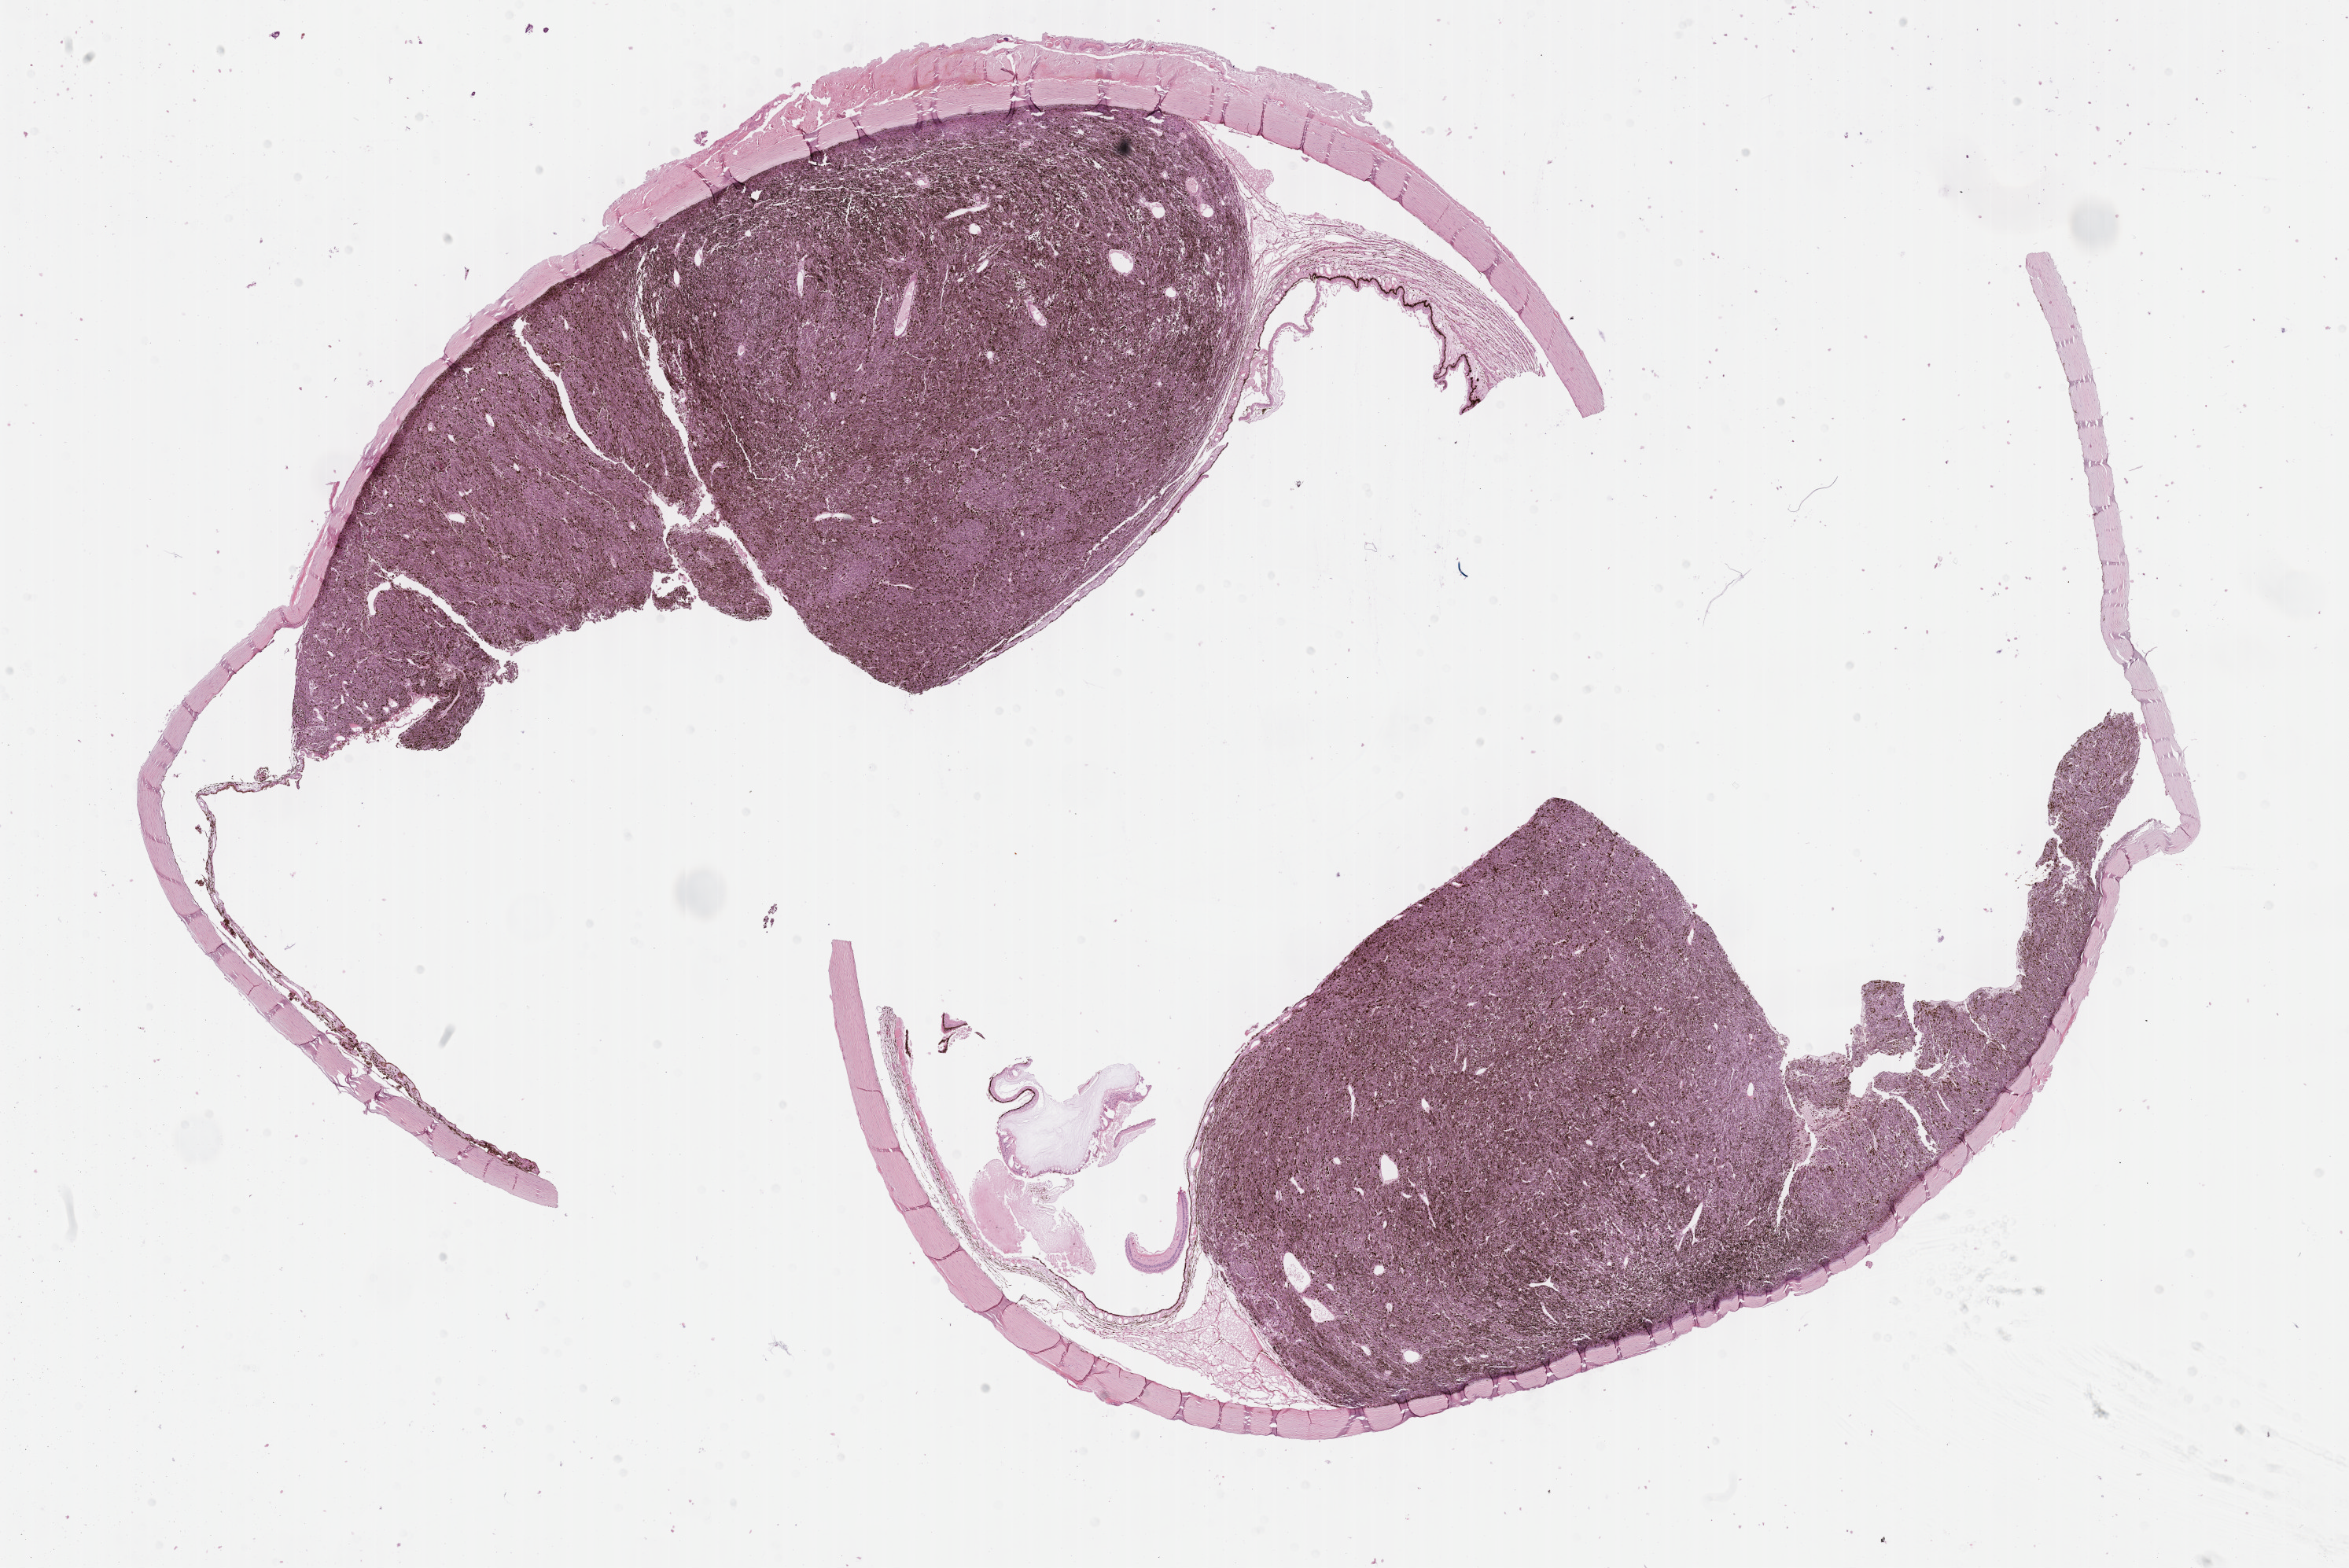
Digitized H&E tissue section (whole slide) — whole scanned area (about 24.2 x 16.1 mm) shown as a low-resolution overview. Formalin-fixed paraffin-embedded (FFPE) diagnostic section. Sample: primary tumour, uvea. Patient: female, age at initial diagnosis 46 years.
- diagnosis: Epithelioid cell melanoma (choroid)
- AJCC pathologic stage: IIB
- laterality: right